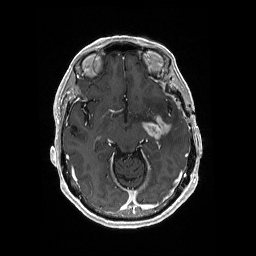
Brain MRI from a brain-tumour surgery series, one axial slice. Position 111 of 176 along the scan axis. T1-weighted post-contrast. 1 mm slice thickness. 256 × 256 image matrix, field of view 256 × 256 mm. From the clinical record (not read from this slice): histopathology: Glioblastoma; WHO grade: 4; IDH mutation: no.
Annotated regions visible in this slice (expert manual segmentation):
- tumour: bounding box (x1, y1, x2, y2) in pixels: (141, 116, 172, 139)